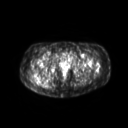
FDG PET of an extremity soft-tissue mass (from a PET/CT study), one axial slice. Position 45 of 267 along the scan axis. 3.27 mm slice thickness. 128 × 128 image matrix, field of view 600 × 600 mm. Female patient, age 60 years. From the clinical record (not read from this slice): histological type: spindle cell suggestive of myxofibrosarcoma; grade: intermediate; site of the primary tumour: right buttock.
Outlined on this slice (expert contour drawn on MRI and transferred to this co-registered scan by the dataset authors):
- gross tumour volume (mass): bounding box [x1, y1, x2, y2] px = [33, 73, 46, 83]